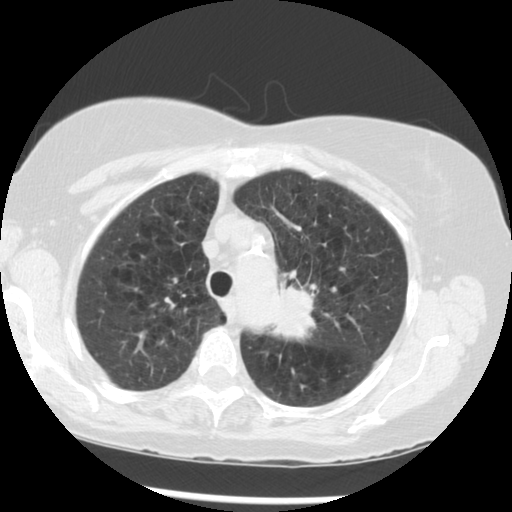
Chest CT (low-dose screening protocol), one axial image; third annual screen; lung window (W 1500 / L -600 HU); standard (soft-tissue) reconstruction kernel (STANDARD); slice 218 of 283 in the series; 512 × 512 image matrix, field of view 330 × 330 mm. Female, age 70 years at enrolment. Current smoker at enrolment.
- Lesion marked by an expert reader, bounding box (x1, y1, x2, y2) in pixels: (264, 270, 358, 359).
- The exam's reader record, not a measurement of the box and not confirmed to be the same lesion: non-calcified nodule or mass ≥4 mm, left upper lobe, 32 × 26 mm, spiculated (stellate) margins, soft tissue attenuation, pre-existing on the prior screen: yes; interval growth: yes.
- Official screen result: positive, other.
- Lung cancer was diagnosed 24 days after this screen: neoplasm, malignant, left upper lobe, stage IIIB (AJCC 6th edition), 40 mm at pathology.